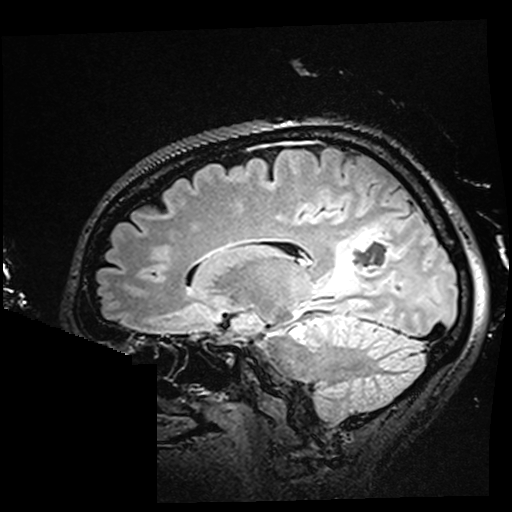
Brain MRI from a brain-tumour surgery series, one sagittal slice; position 106 of 176 along the scan axis; T2 FLAIR; 512 × 512 image matrix, field of view 250 × 250 mm. Case-level facts recorded for this patient, not image findings: histopathology: Oligodendroglioma; WHO grade: 2; IDH mutation: yes.
Structures marked on this image (outlined manually by an expert reader):
- residual tumour: bounding box [x1, y1, x2, y2] px = [323, 231, 373, 297]